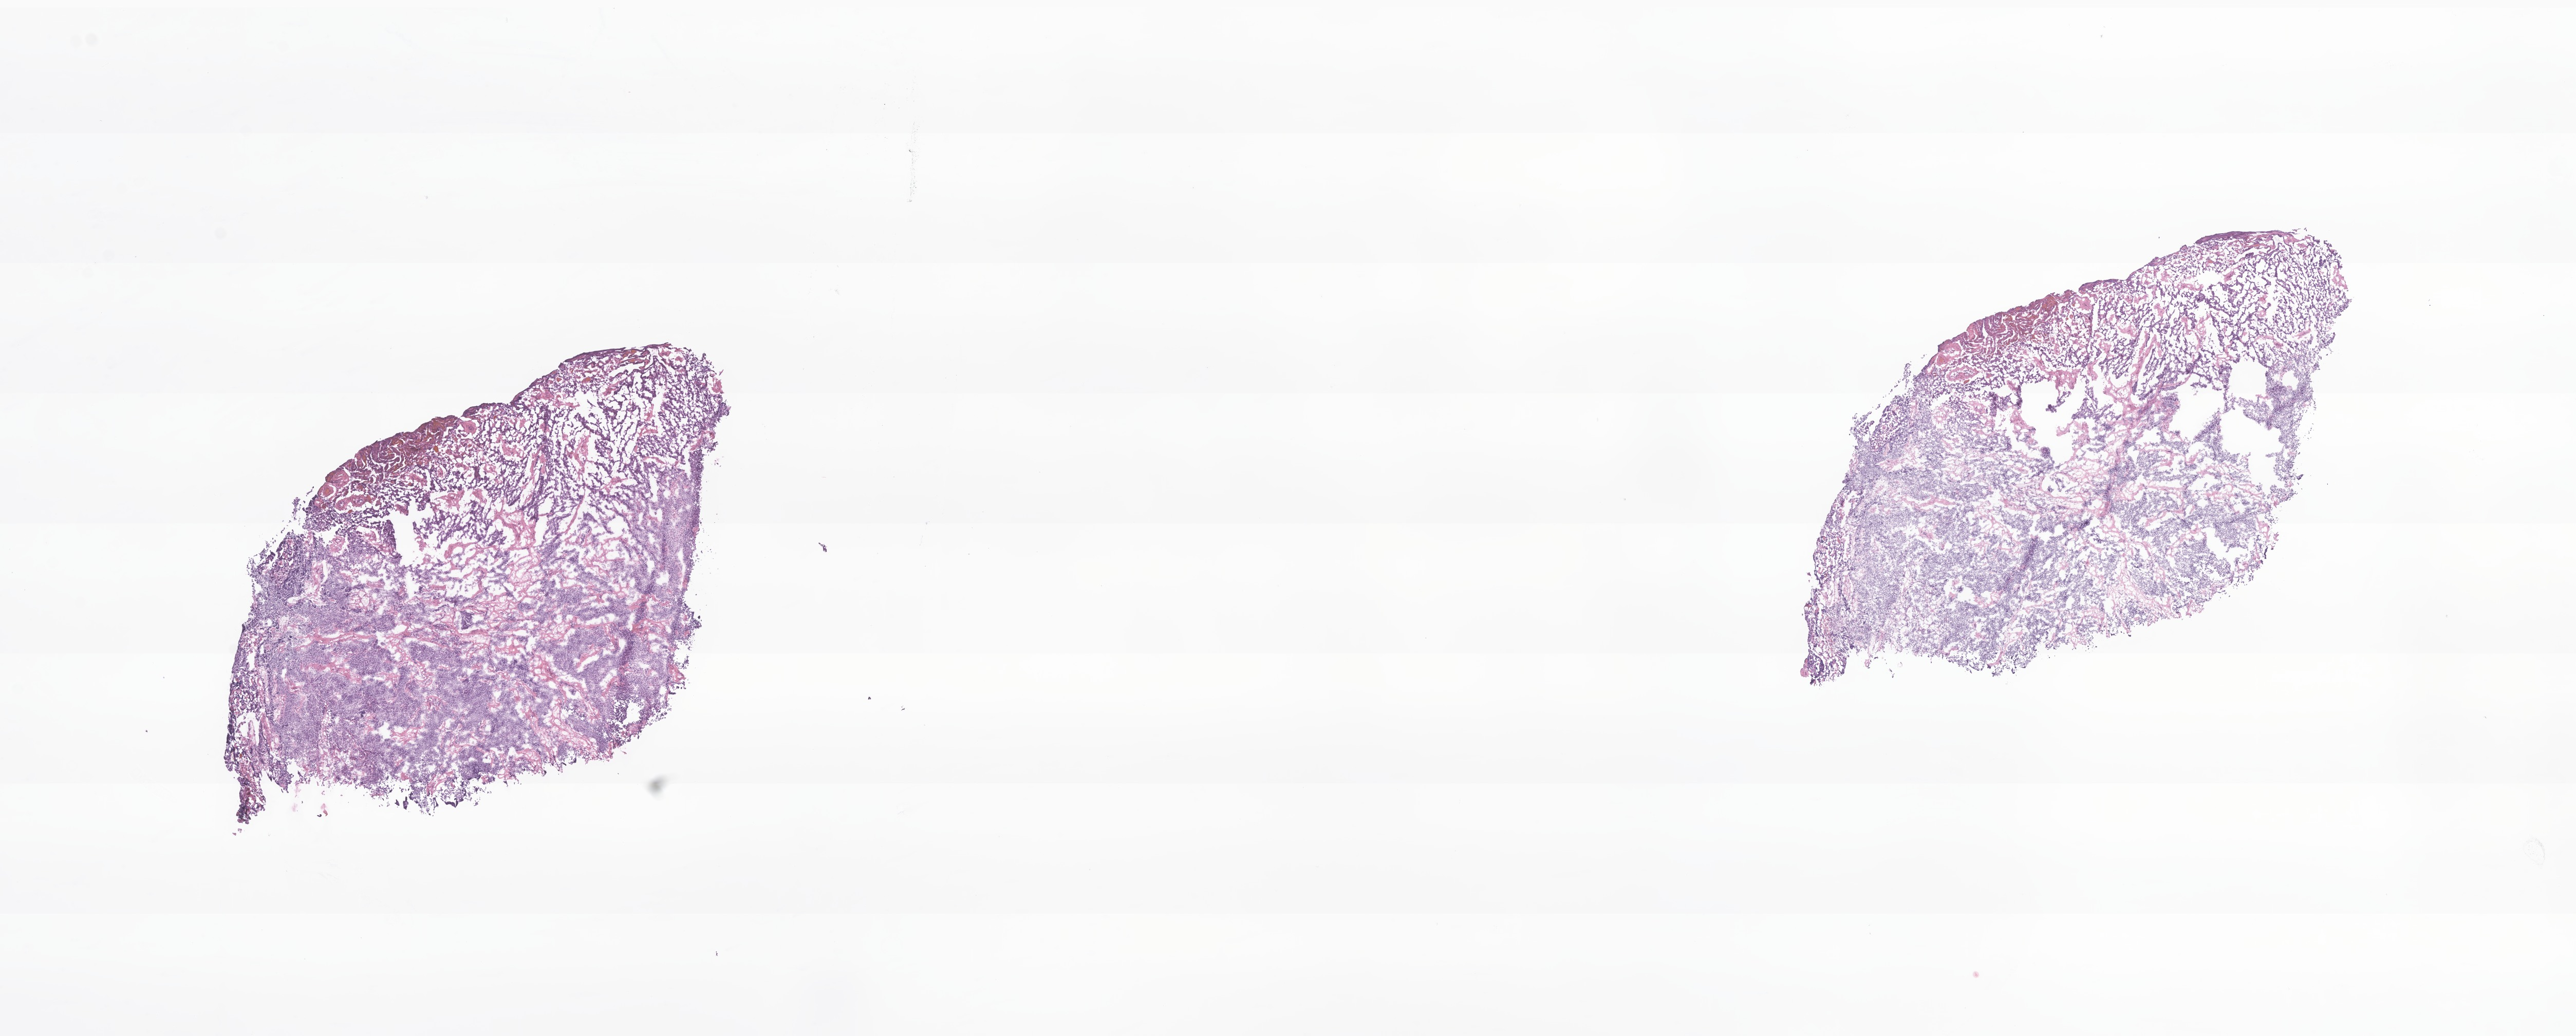
H&E whole-slide image of tumor tissue from the cerebral ventricle, low-resolution overview of the scanned area, about 21.1 x 8.5 mm. Frozen section. Patient female; age 77 months (6 years 5 months).
Recorded diagnosis: Medulloblastoma, NOS.